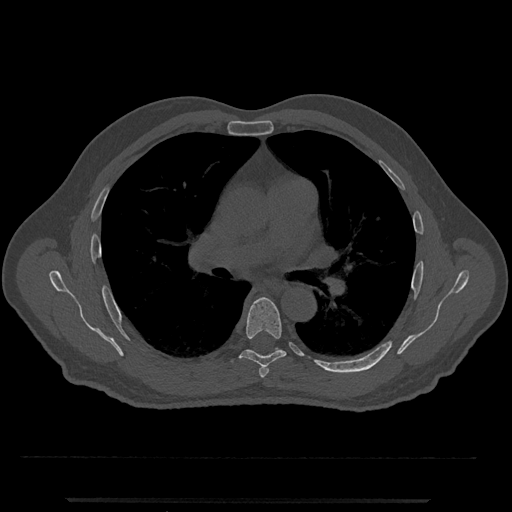
CT including the spine, one axial slice. Slice 736 of 797 in the series (ordered by position). Bone window (W 1800 / L 400 HU). 0.5 mm slice thickness. 512 × 512 image matrix. Patient: male, 63 years. Case-level facts recorded for this patient, not image findings: primary cancer: prostate.
Annotated regions visible in this slice (semi-automatically segmented with operator editing):
- T5 vertebra: bounding box <259,365,269,378> (left, top, right, bottom; pixels)
- T6 vertebra: <239,297,286,367>
- T7 vertebra: <275,348,277,350>